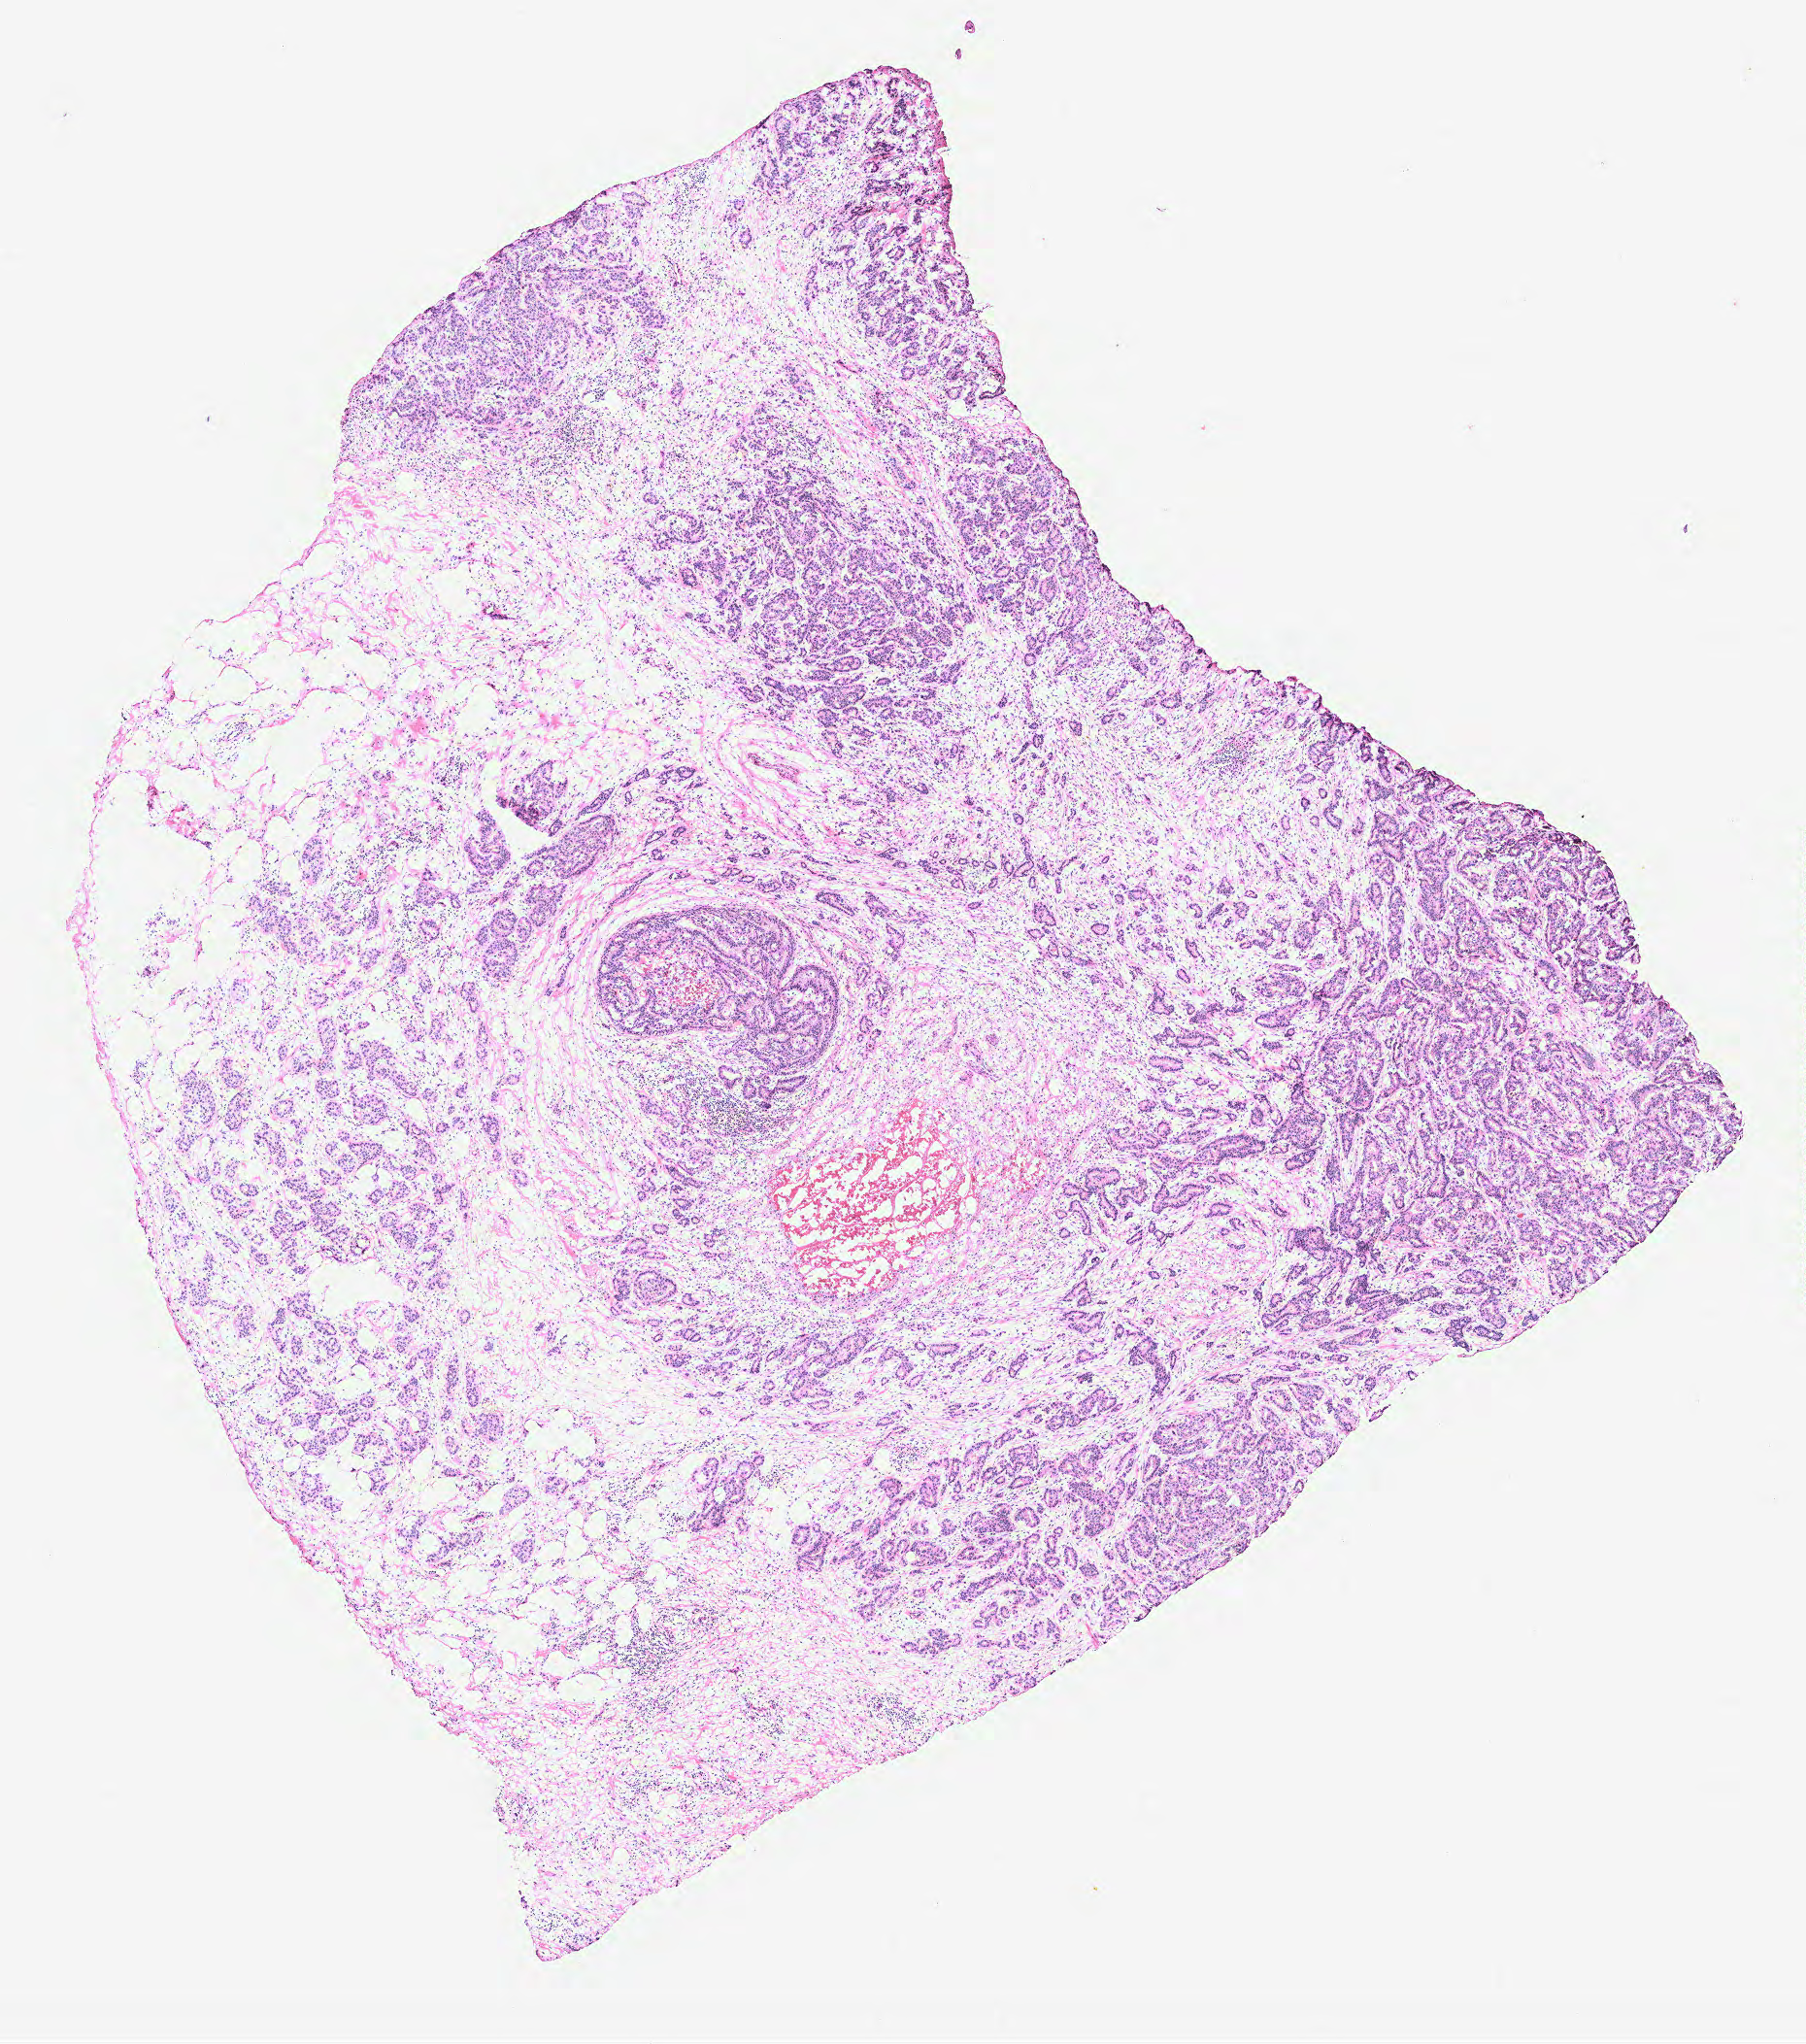
H&E-stained whole-slide image — low-resolution overview of the scanned area, about 7.4 x 8.4 mm (slide scanned at 40x); breast, tumour tissue. Patient: female, age 55 years.
Histologic diagnosis: Infiltrating duct carcinoma, NOS. AJCC pathologic stage: IIIA.